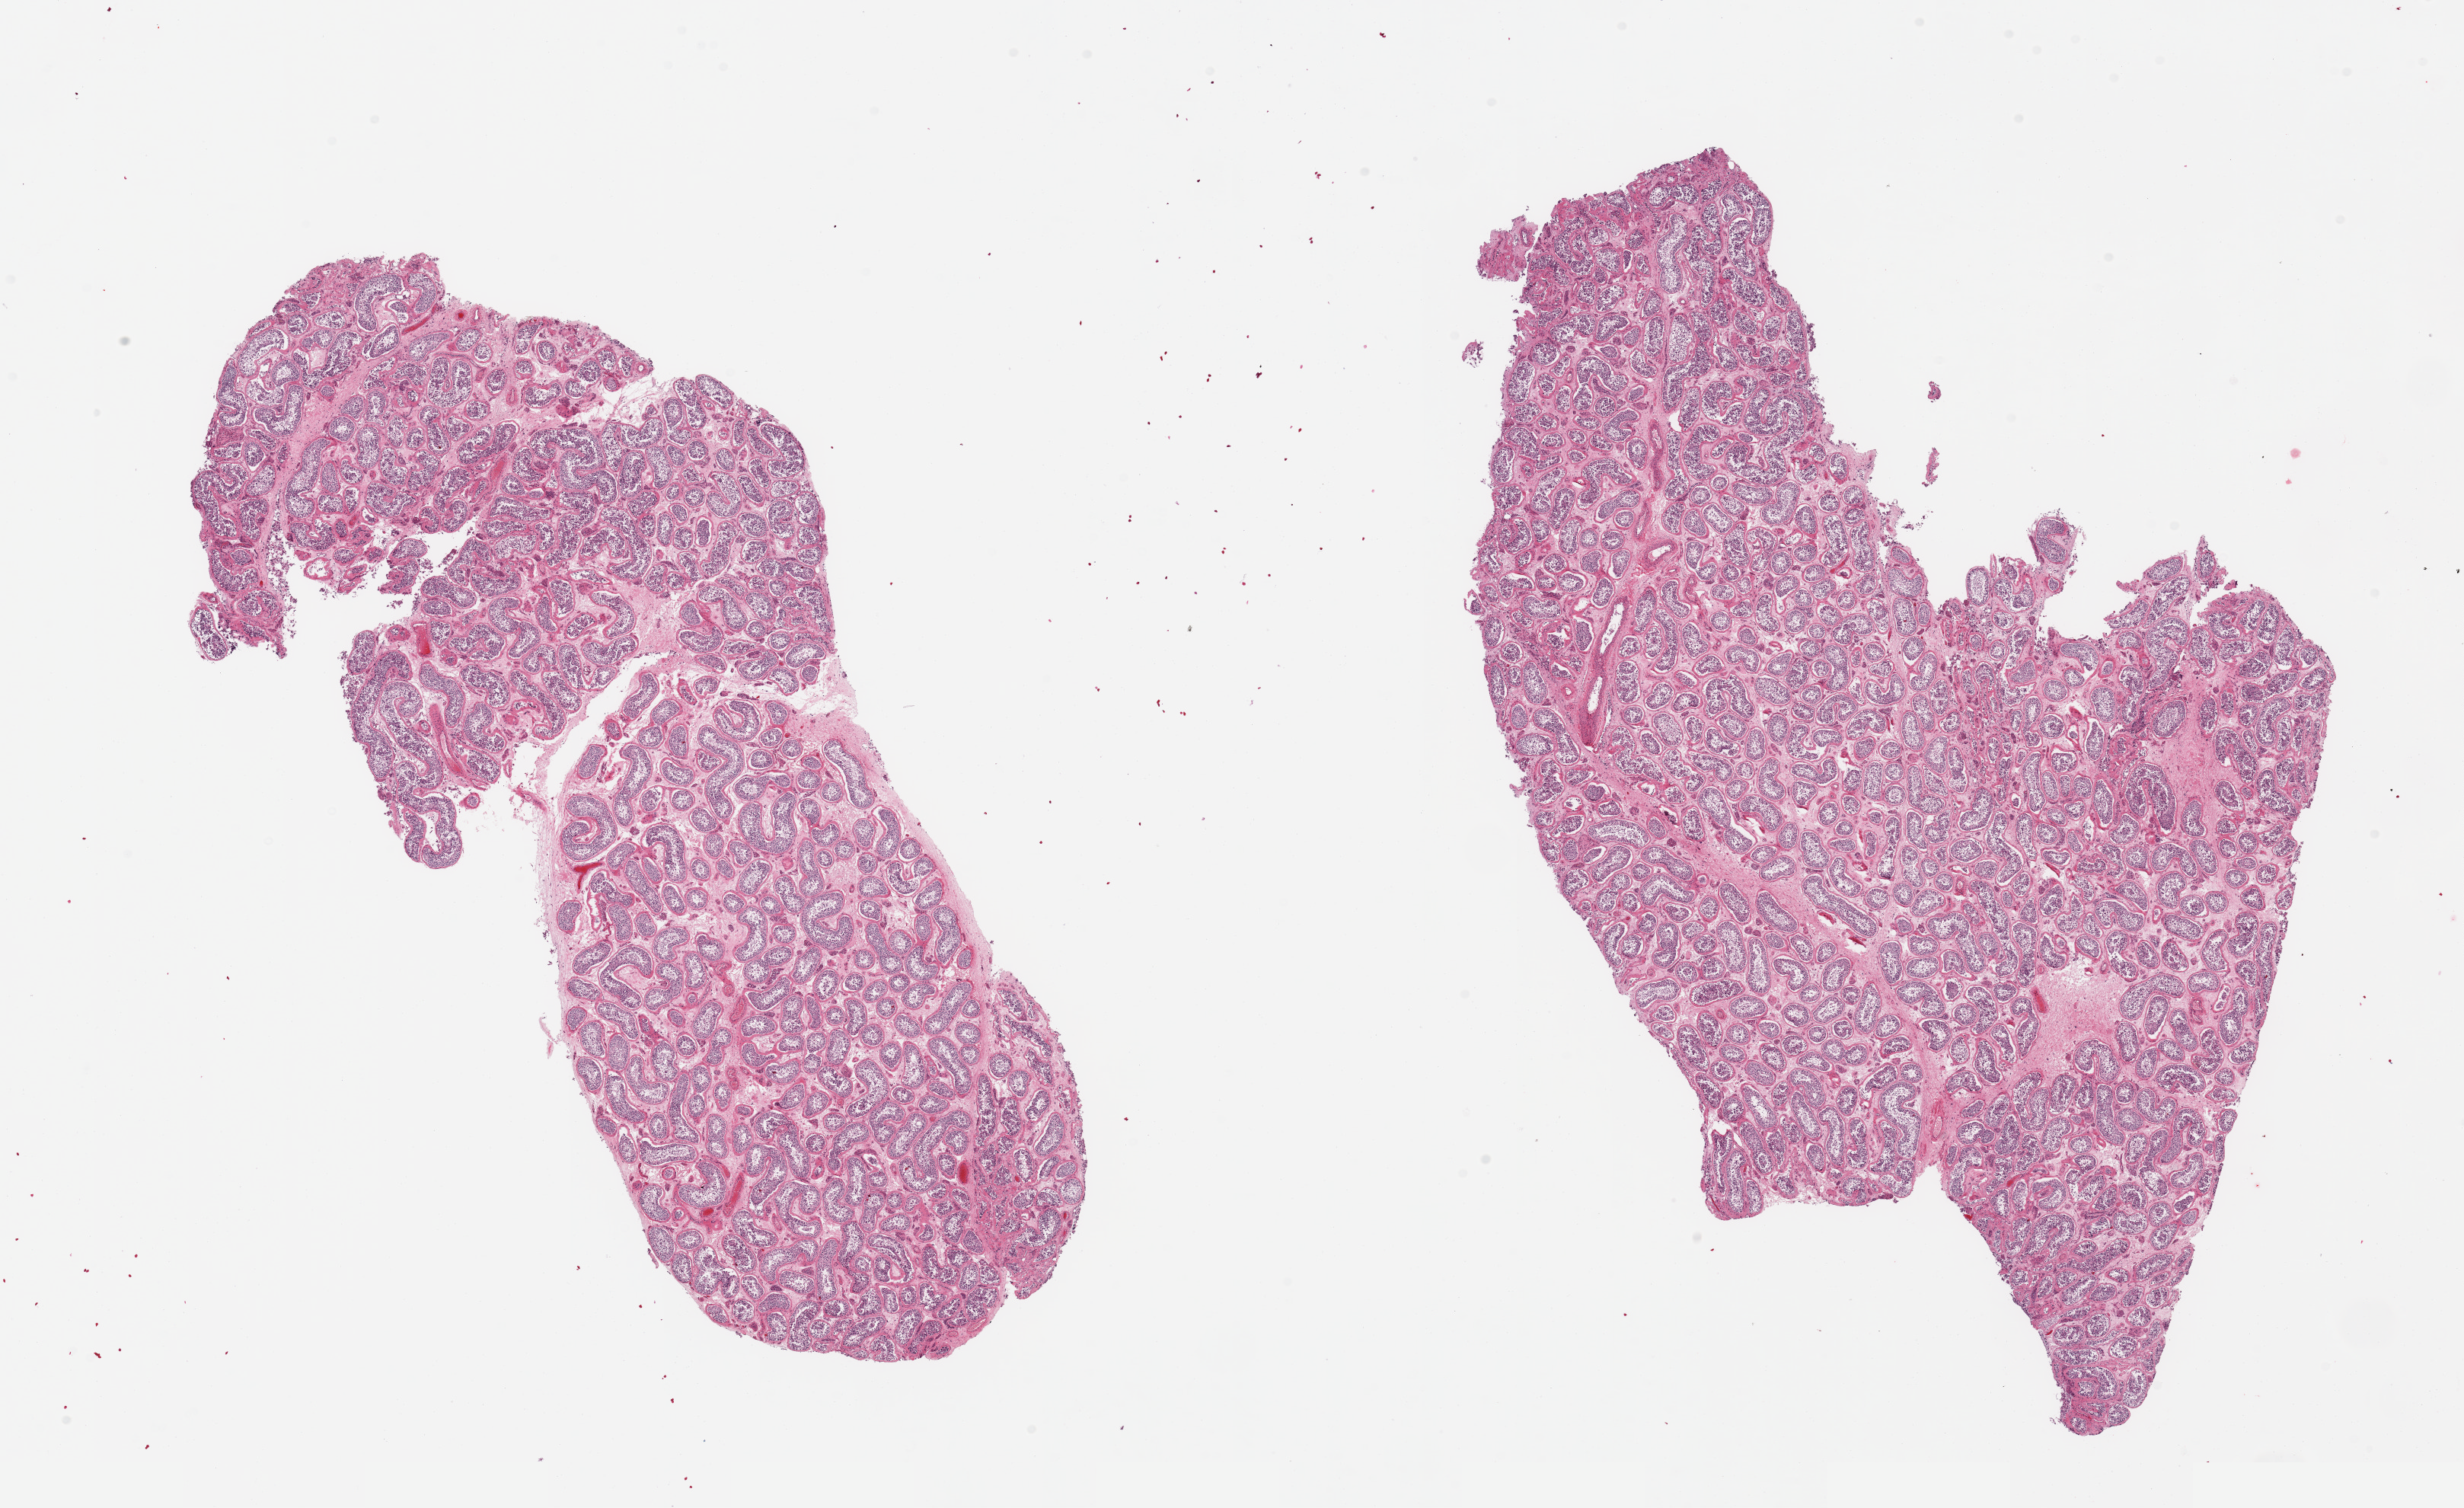
Whole-slide image, H&E stain — a low-resolution overview of the entire scanned area, about 25.6 x 15.7 mm, PAXgene-fixed paraffin-embedded (PFPE) section, section of testis (target tissue), tissue donor sample. Male donor.
Reviewer comment on this tissue sample: 2 pieces, spermatogenesis is present.